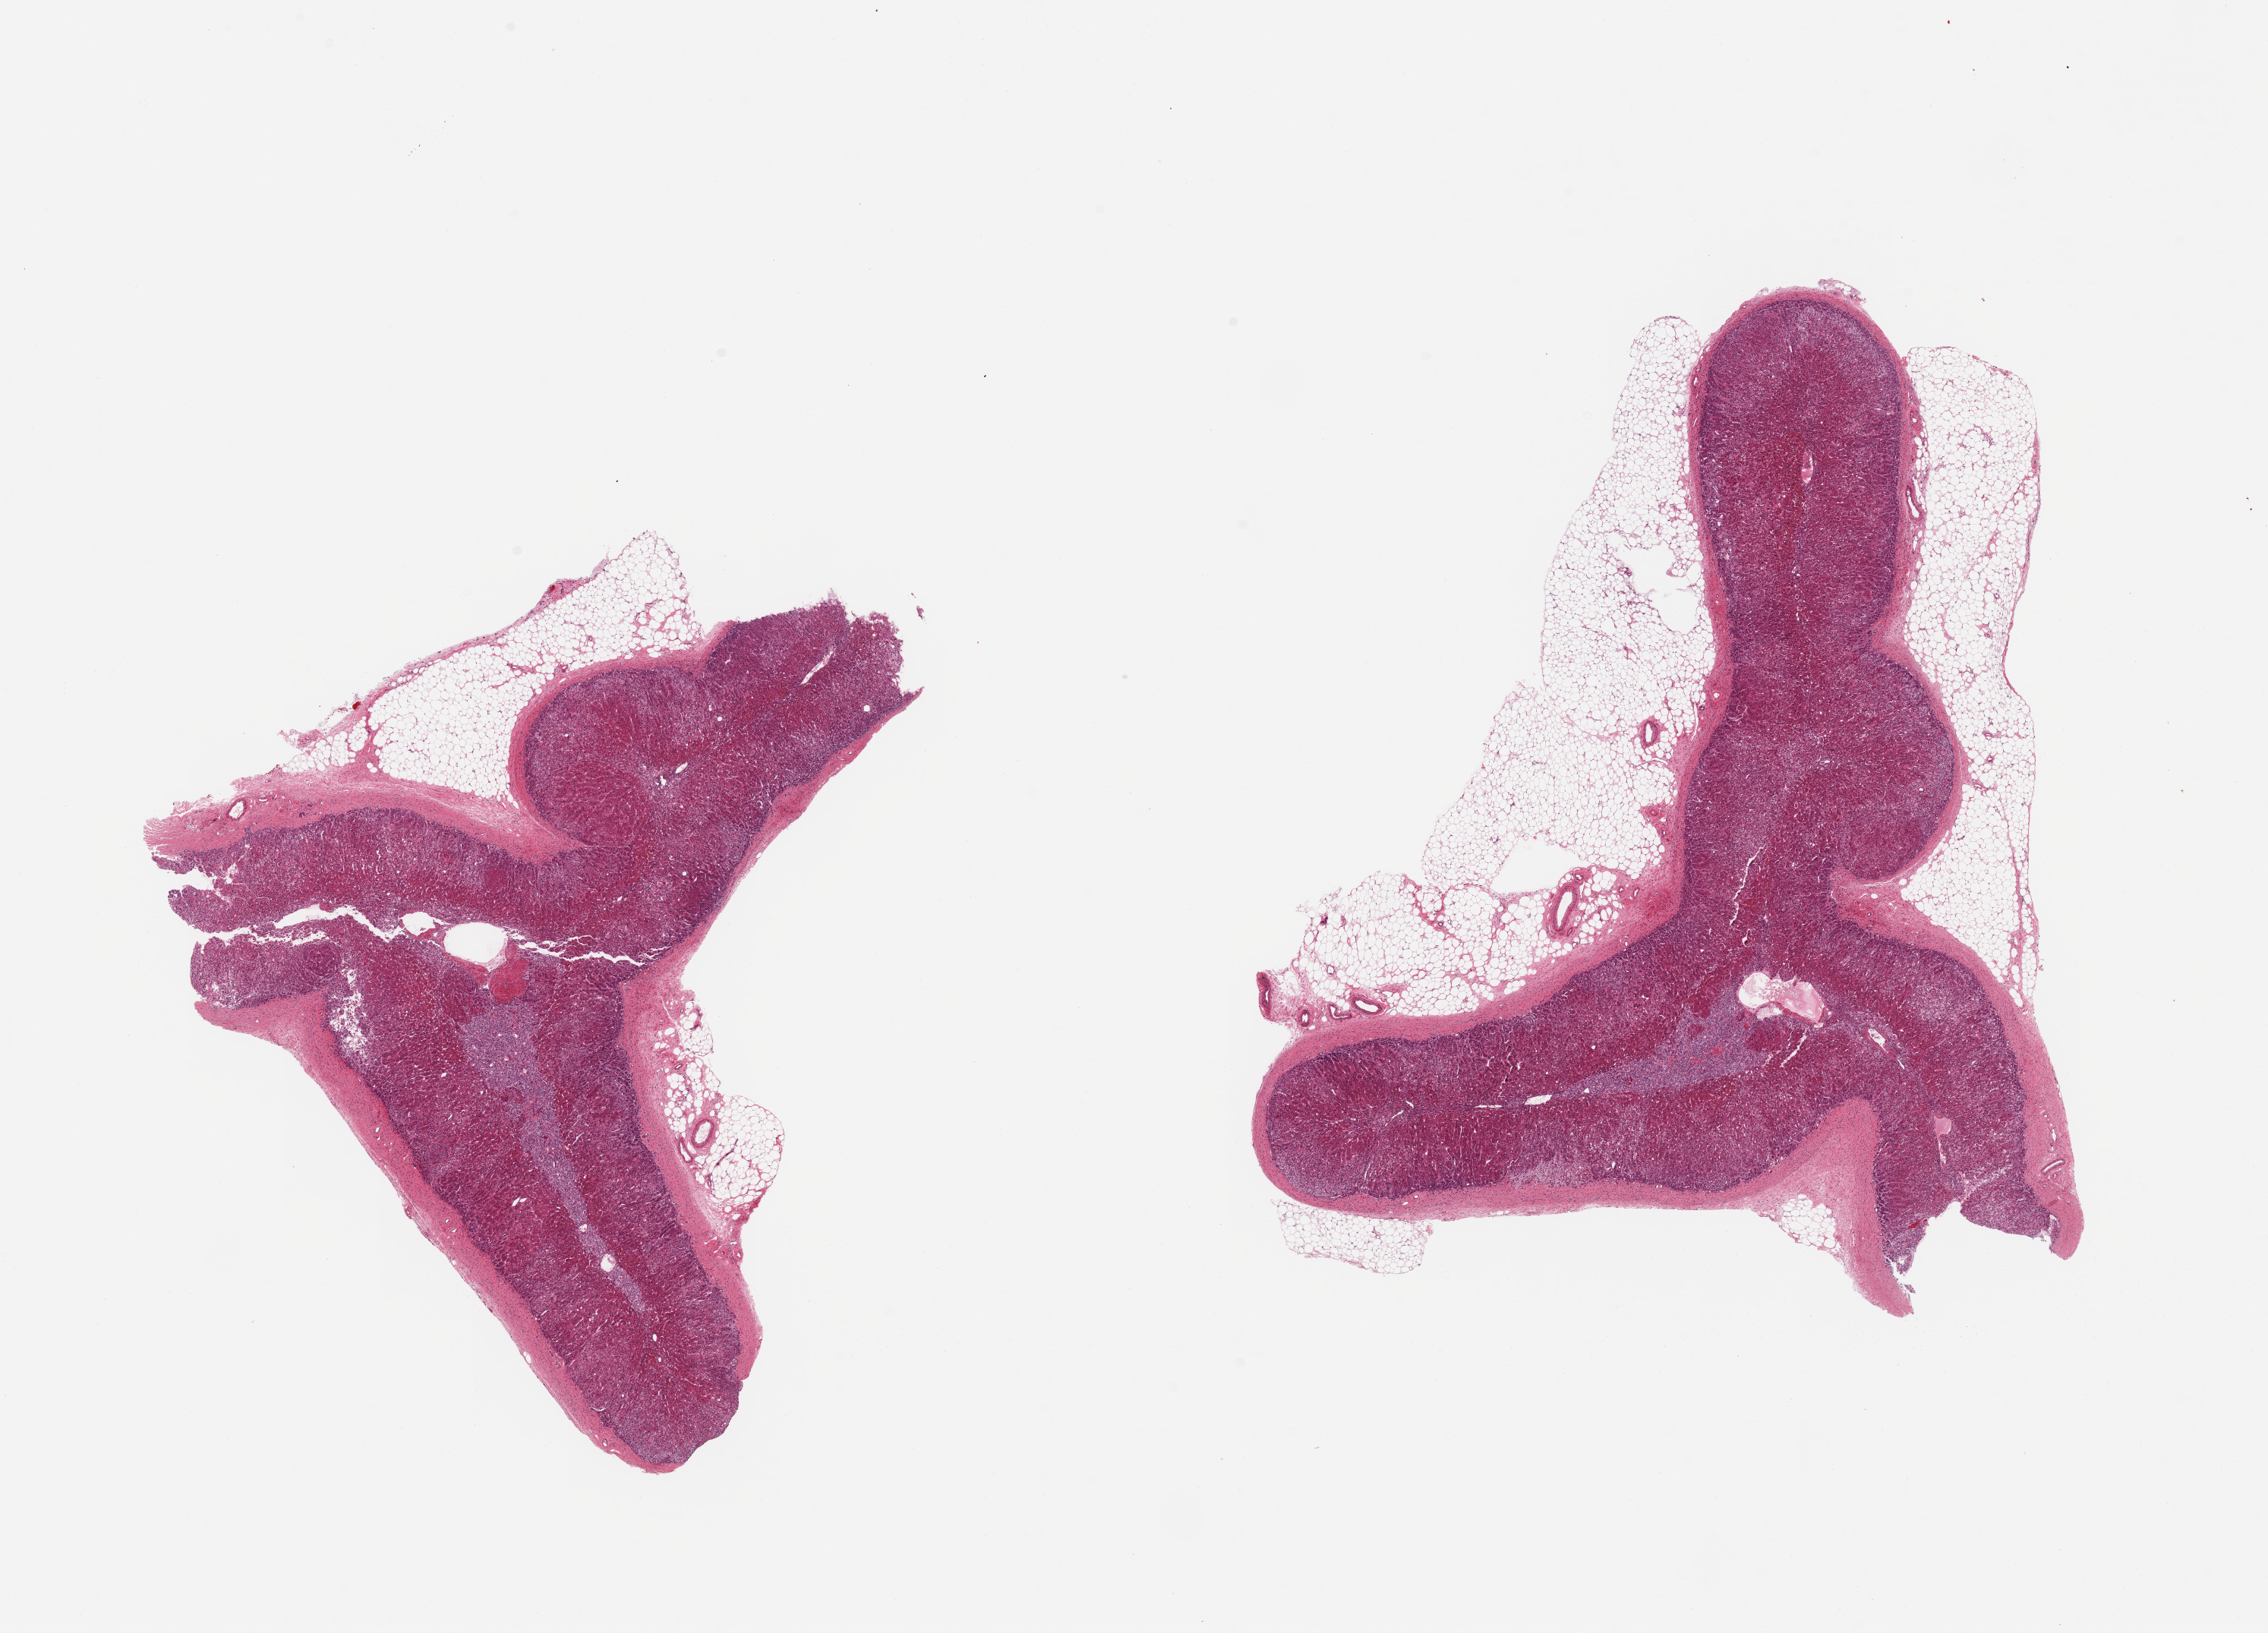
Whole-slide image, H&E stain, brightfield — whole scanned area (about 23.6 x 17.0 mm) shown as a low-resolution overview; PAXgene-fixed, paraffin-embedded tissue; section of adrenal gland (target tissue); donor tissue sample. Donor sex: male.
Pathologist's review note for this sample: 2 pieces, excellent preservation; cortex AND medulla present up to ~2mm focus, valuable specimen, latter, adherent fat by interrupted line.